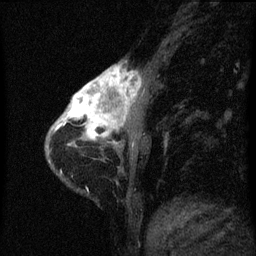
Breast MRI (dynamic contrast-enhanced), one sagittal slice. Slice 13 of 60 in the series (ordered by position). Dynamic contrast-enhanced series, image 2 of 3 at this slice position (ordered by acquisition). 1.5 T. TE 4.2 ms, TR 8 ms. 2 mm slice thickness. 256 × 256 image matrix. Patient: female, 38 years.
Annotated regions visible in this slice (semi-automatically segmented with operator editing):
- analysis volume of interest (the breast-tissue region the enhancement analysis was run in; not a lesion): box from (x=61, y=66) to (x=142, y=147) px
- tumour enhancement mask (voxels above the 70 % enhancement threshold inside the analysis volume of interest): (x=61, y=66)–(x=140, y=147)